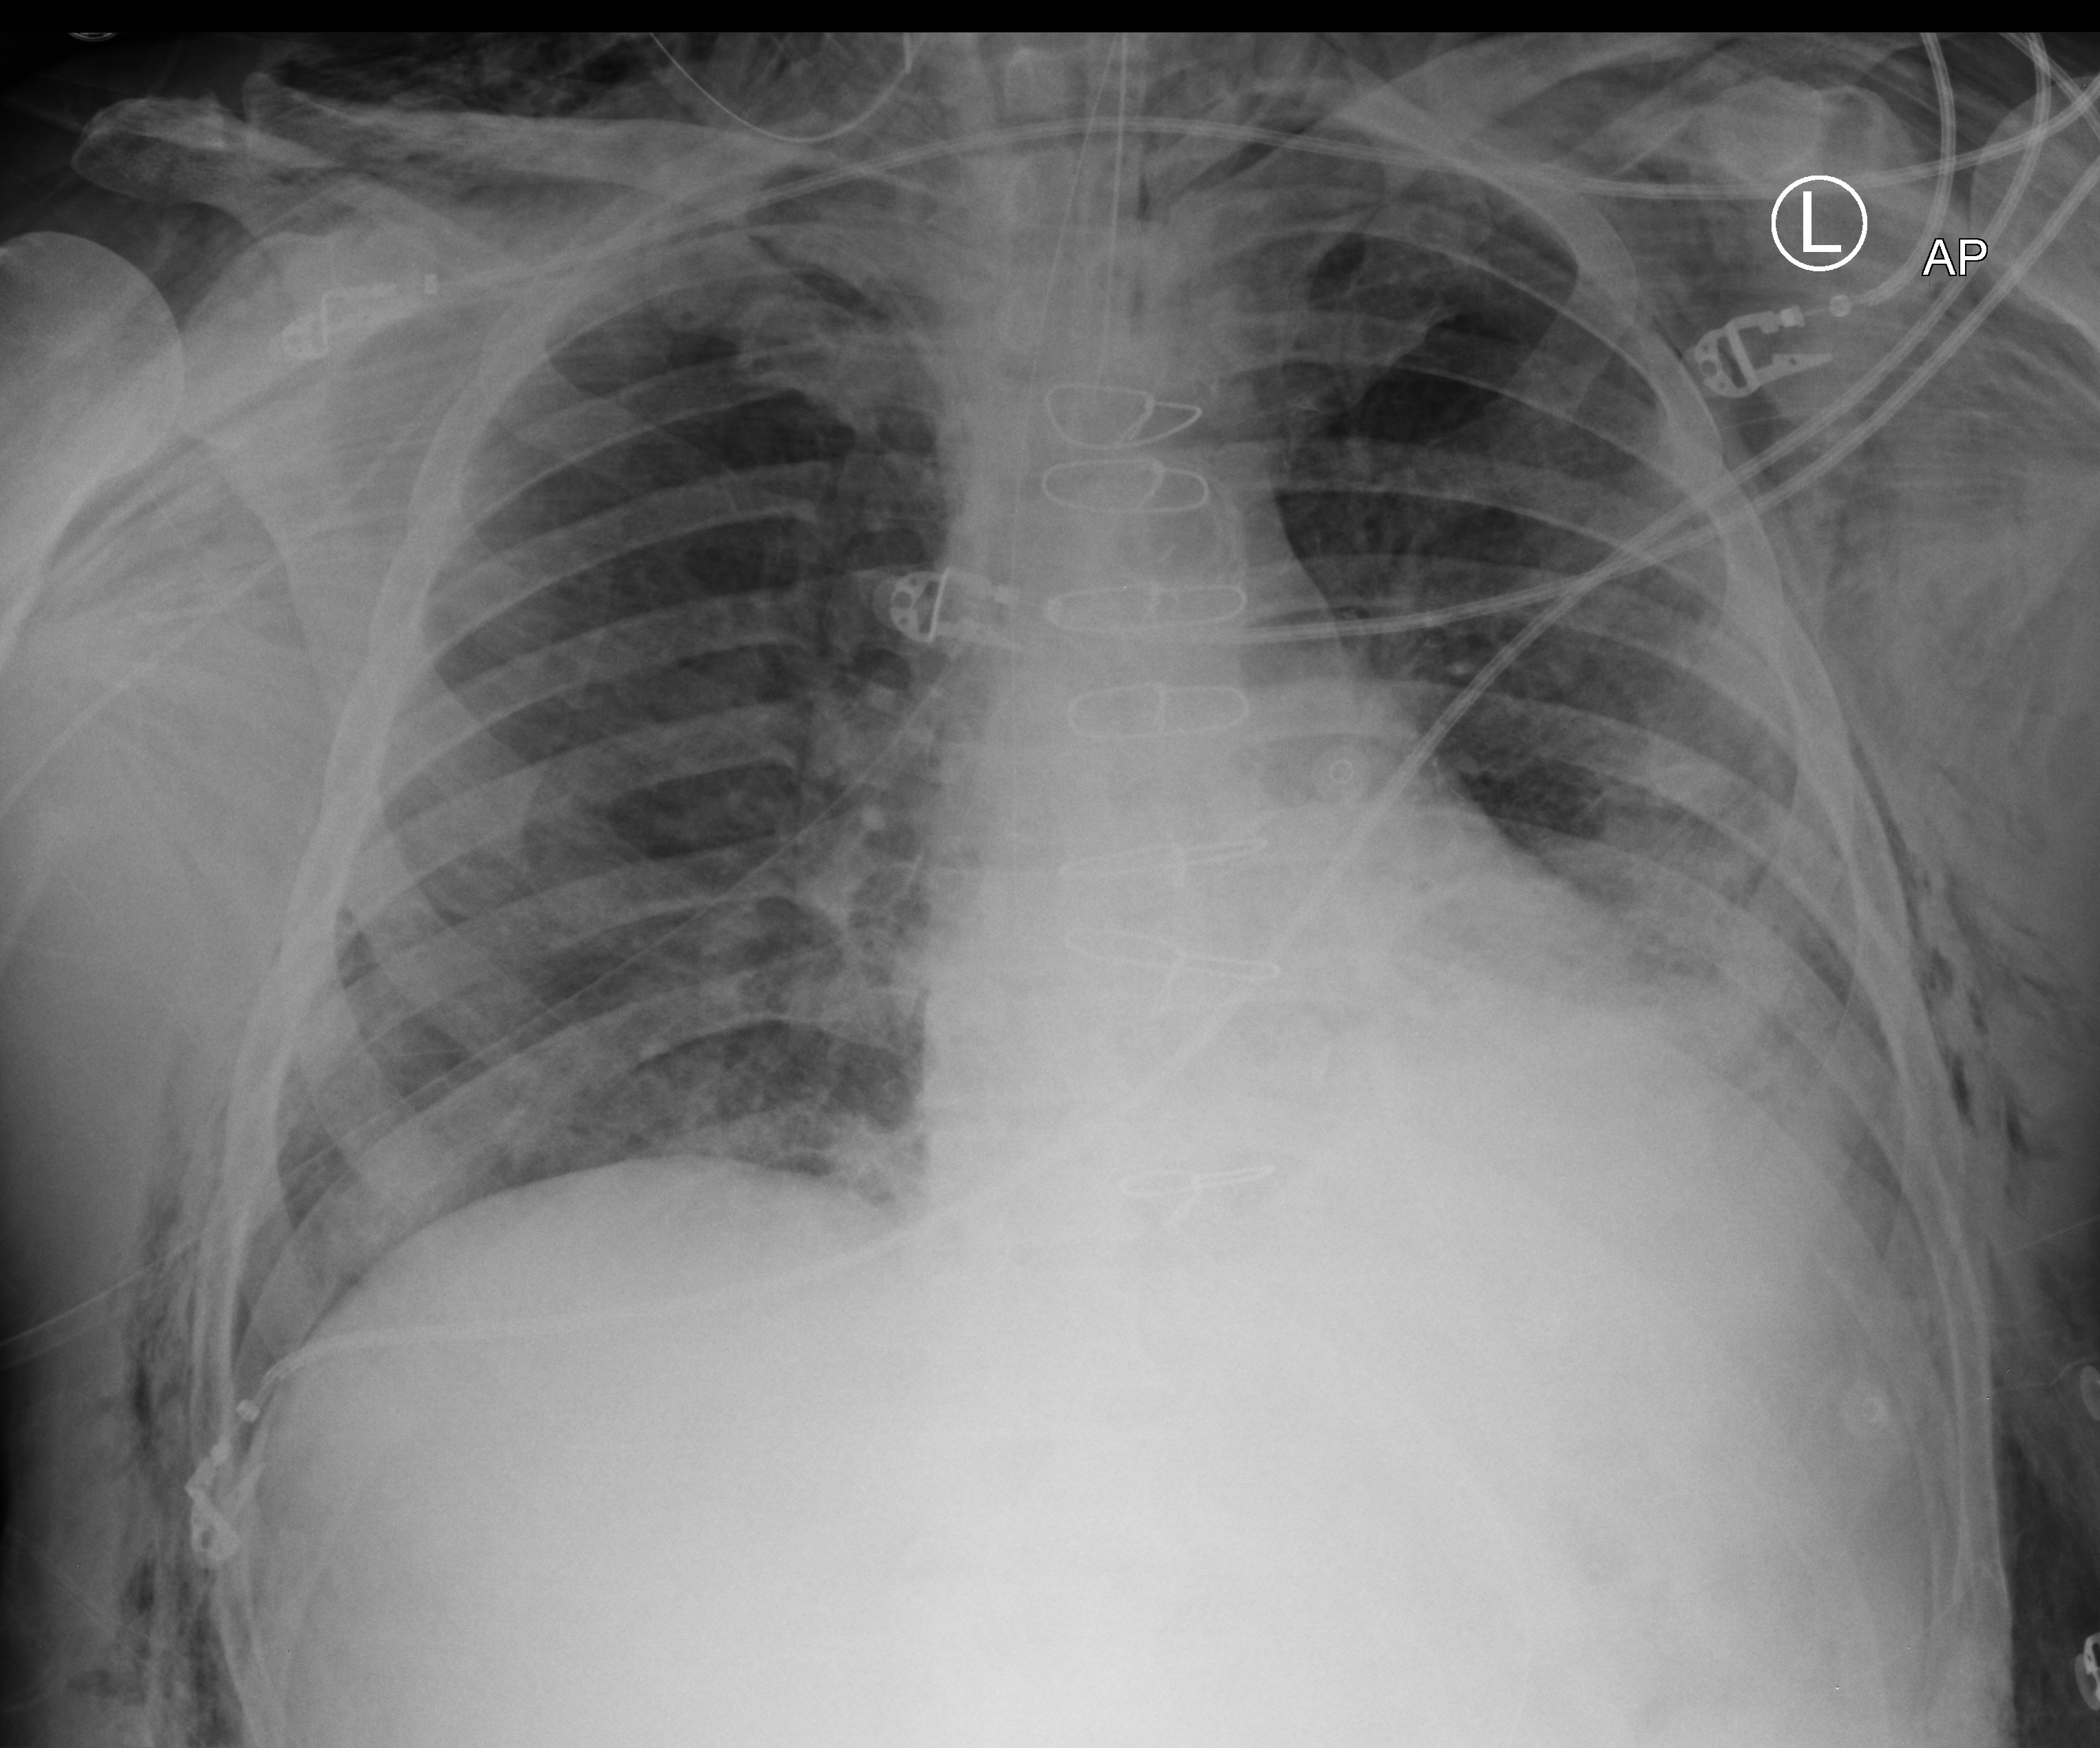
Chest X-ray (portable), anteroposterior (AP) projection. Patient hospitalised with COVID-19; male, aged 60–74 years.
Admission-level facts for this patient (not findings on this image; timing relative to this image not recorded): admitted to intensive care during this hospital stay: yes; hypertension (admission record): yes; other chronic lung disease (admission record): no.